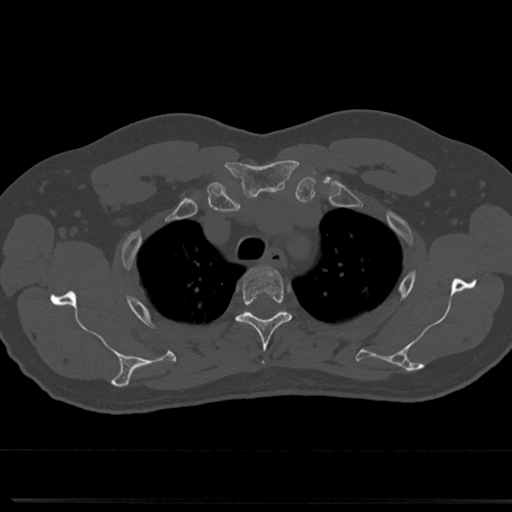
CT including the spine, one axial slice. 120 kVp. Bone window (W 1800 / L 400 HU). 0.5 mm slice thickness. 512 × 512 image matrix. Male patient, age 61 years. Case-level facts recorded for this patient, not image findings: primary cancer: prostate.
Annotated regions visible in this slice (semi-automatically segmented with operator editing):
- T3 vertebra: bounding box (x1, y1, x2, y2) in pixels: (237, 267, 292, 366)